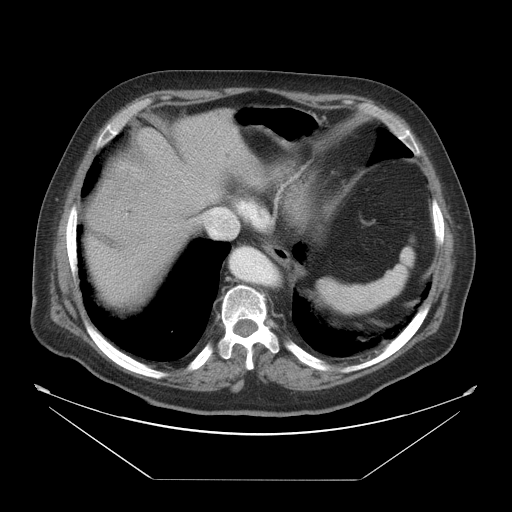
Contrast-enhanced abdominal CT, one axial slice. Slice 42 of 45 in the series (ordered by position). 120 kVp. Intravenous contrast given. Soft-tissue window (W 400 / L 40 HU). 512 × 512 image matrix. Male patient, age 87 years. From the clinical record (not read from this slice): diagnosis: colorectal cancer liver metastases, imaged before liver resection; multiple liver metastases: no; largest metastasis: 4.5 cm; disease in both lobes: yes.
Structures marked on this image (manually delineated by an expert):
- liver: bounding box [x1, y1, x2, y2] px = [85, 110, 262, 312]
- planned liver remnant (the part of the liver to remain after resection): [120, 110, 262, 210]
- liver metastasis: [101, 169, 145, 203]